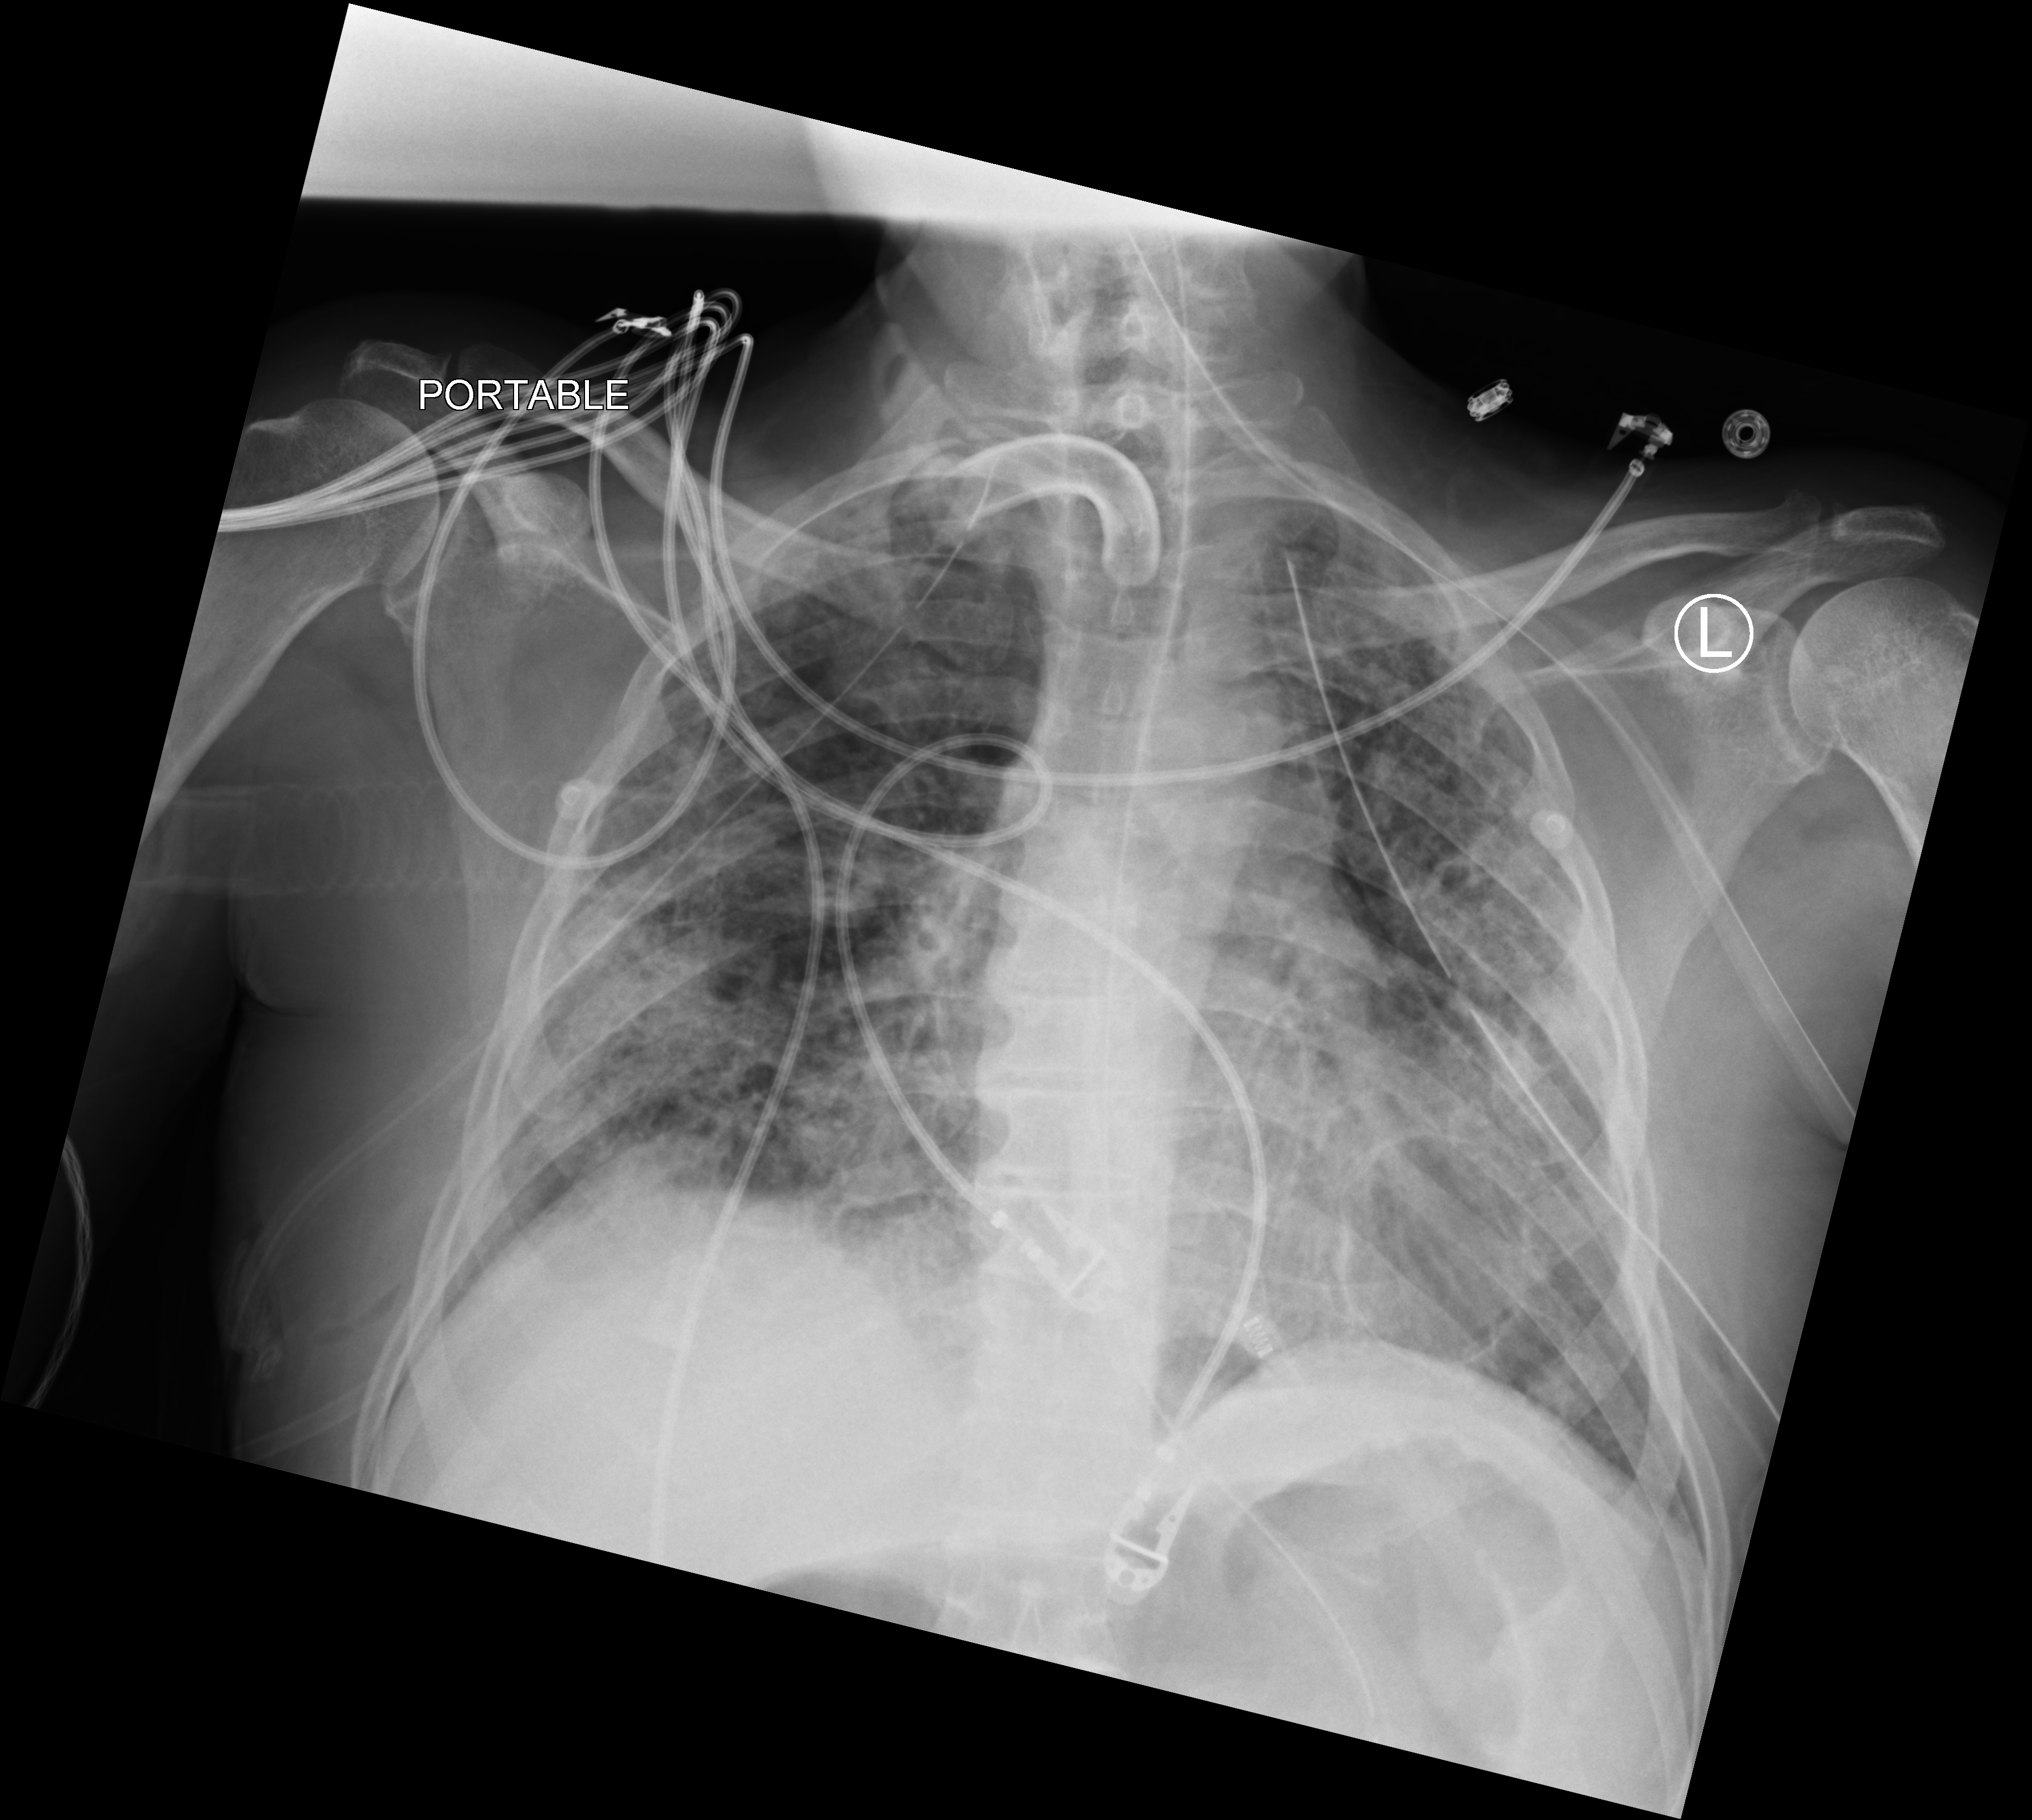
Chest X-ray (portable), anteroposterior (AP) projection. Patient hospitalised with COVID-19; male, aged 18–59 years.
Hospital-stay facts (about this admission, not read from this image; timing relative to this image not recorded):
- diabetes (admission record): no
- mechanically ventilated during this hospital stay: yes